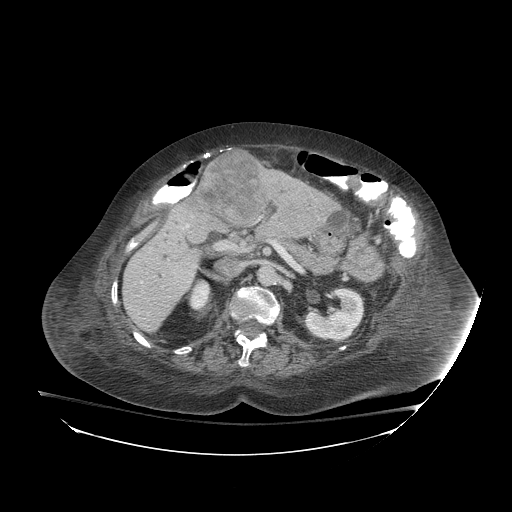
Contrast-enhanced abdominal CT (liver protocol), one axial slice. Position 39 of 81 along the scan axis. Soft-tissue window (W 400 / L 40 HU). 2.5 mm slice thickness. 512 × 512 image matrix. Case-level facts recorded for this patient, not image findings: diagnosis: hepatocellular carcinoma (patient treated with transarterial chemoembolisation; whether this scan precedes or follows treatment is not stated here); TNM stage (as recorded): Stage-I; Child-Pugh class: B.
Outlined on this slice (semi-automatic segmentation, software-assisted and operator-edited):
- liver parenchyma outside the tumour (the mass and vessels are separate outlines, so this box may not span the whole liver): bounding box <122,176,338,332> (left, top, right, bottom; pixels)
- mass: <199,150,268,226>
- liver vessels: <141,224,190,284>